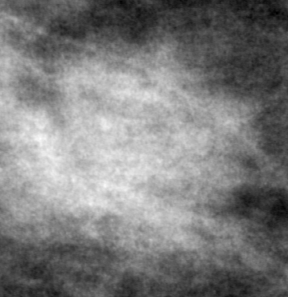
Crop from a digitized film mammogram around one marked abnormality; right breast; MLO view; BI-RADS breast density category 1 (scale 1–4).
Marked abnormality: mass, shape irregular, margins ill defined; BI-RADS assessment category 5; subtlety rating 5 on a 1 (subtle) to 5 (obvious) scale; pathology (as recorded): malignant.